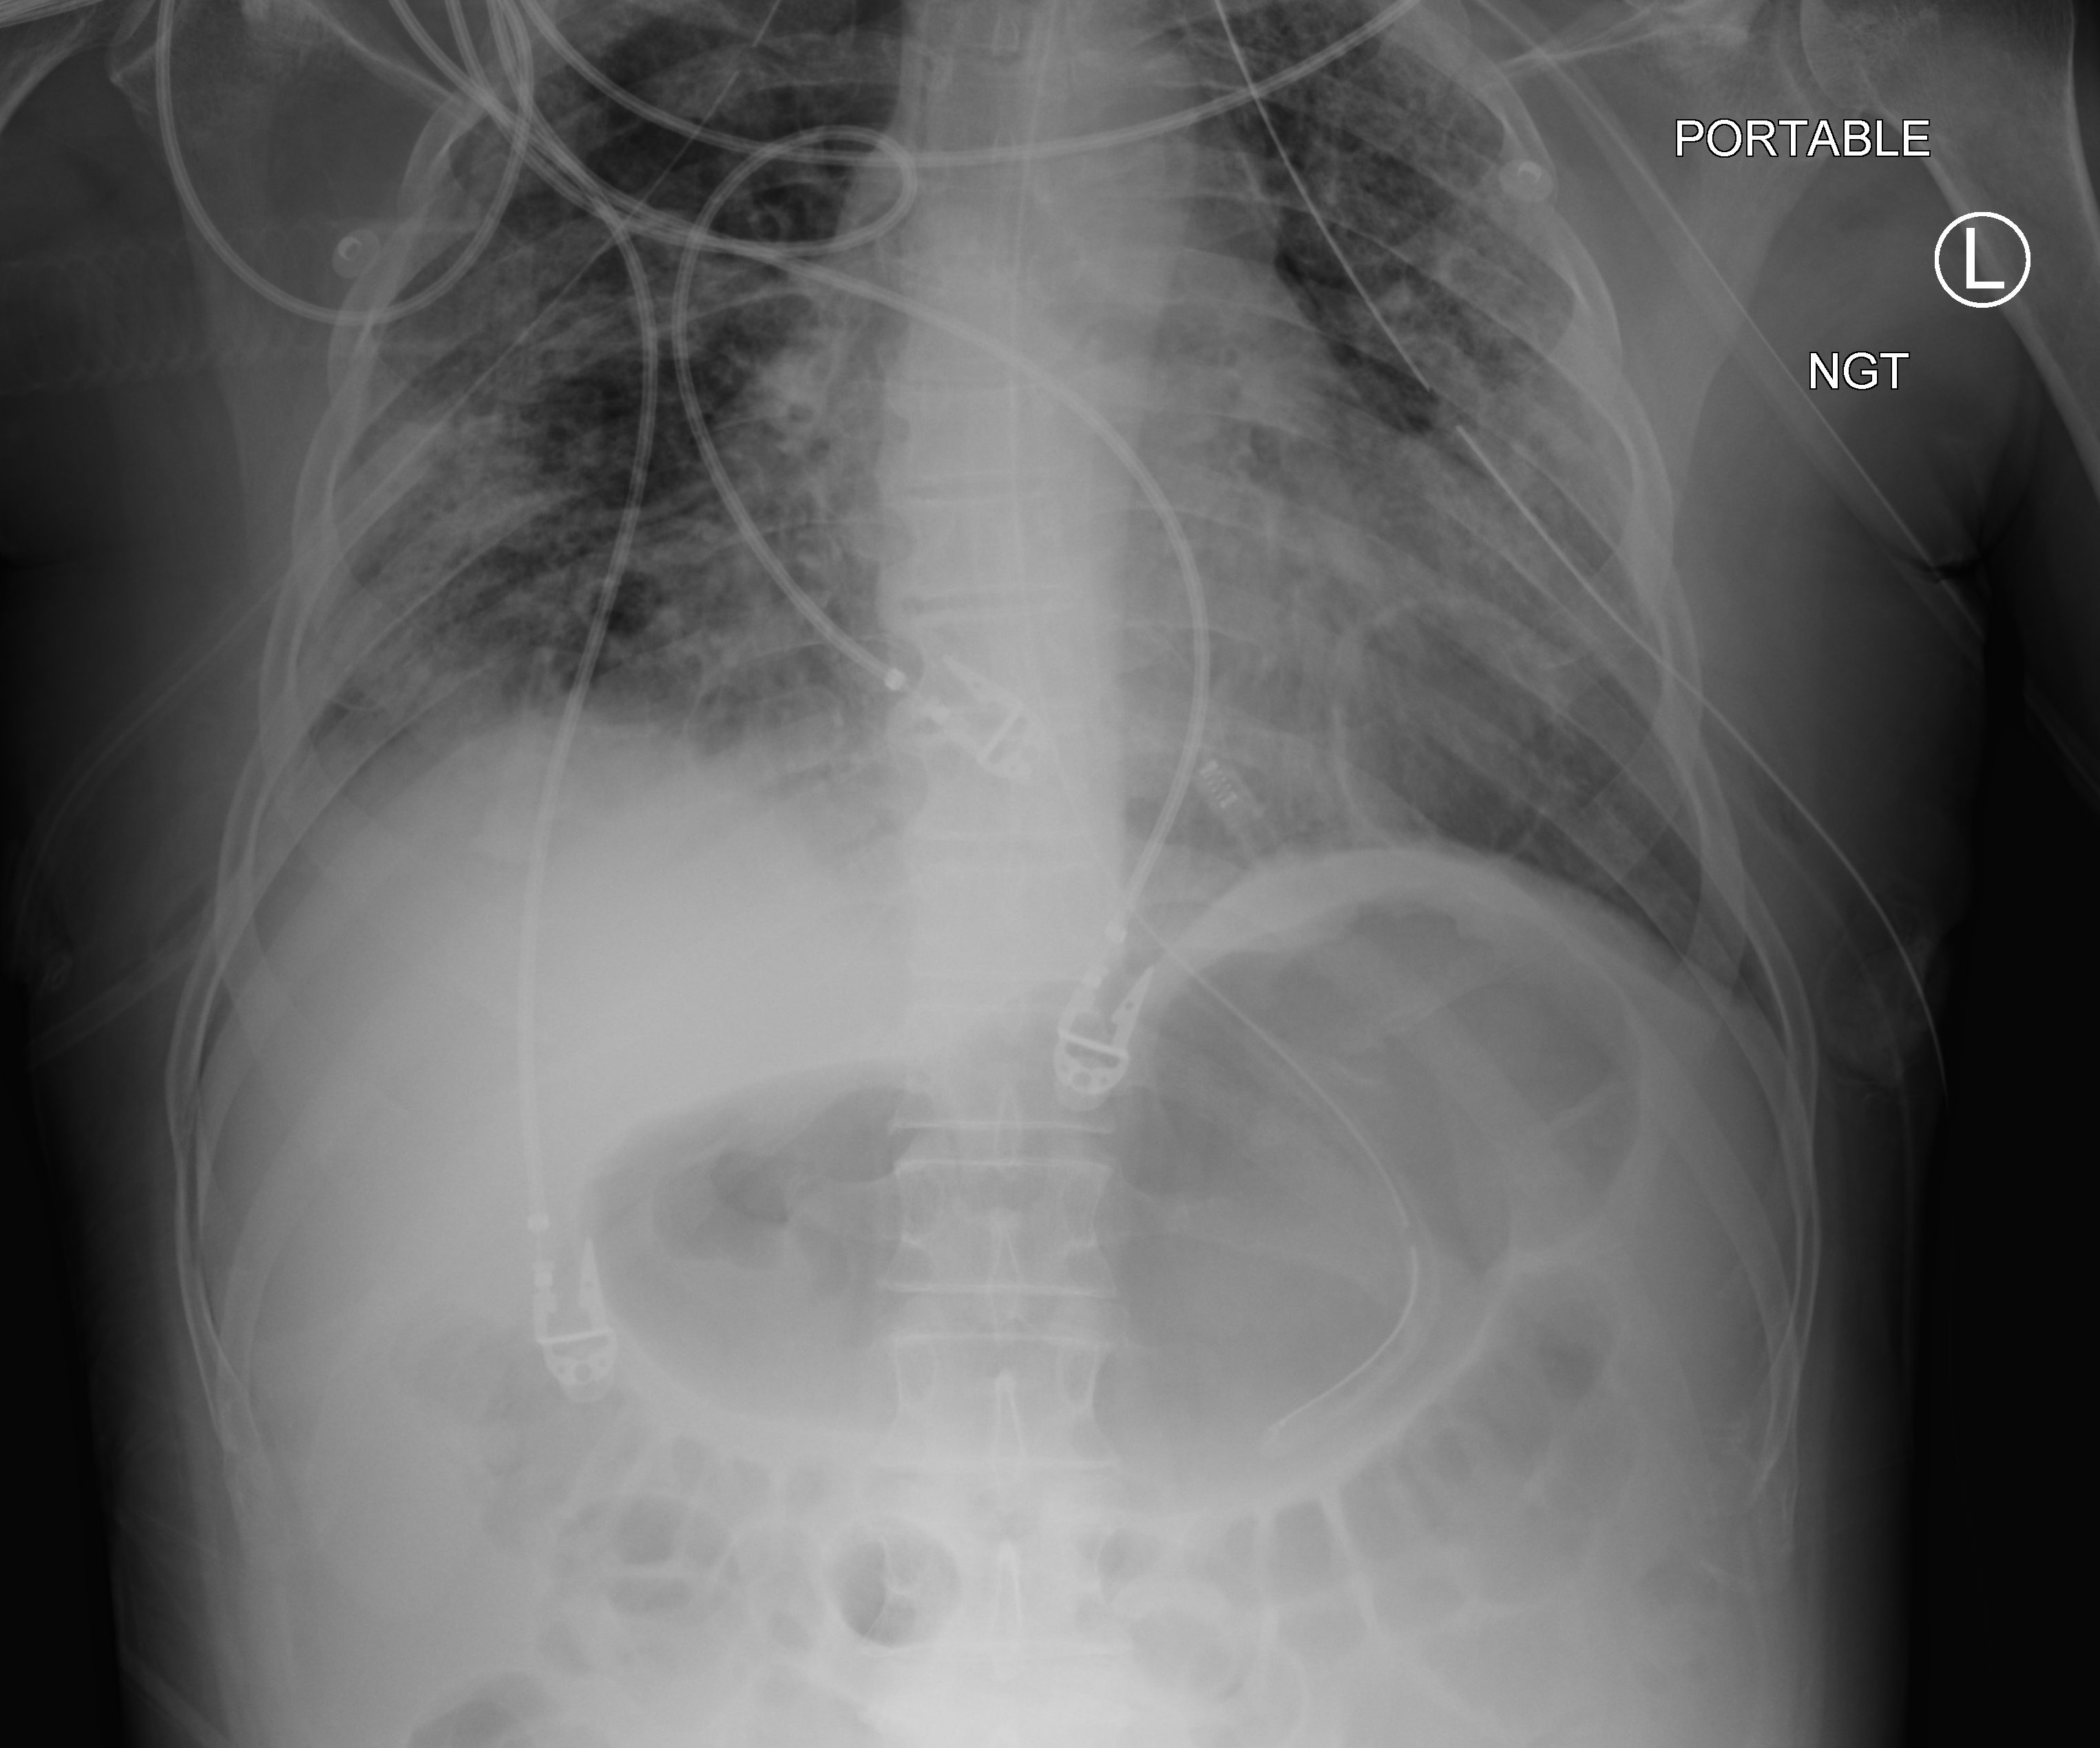
Bedside chest radiograph (computed radiography), anteroposterior (AP) projection. Male patient hospitalised with COVID-19, age 18–59 years.
From the hospital-stay record, not from the radiograph (when in the stay this image was taken is not recorded):
- admitted to intensive care during this hospital stay: yes
- mechanically ventilated during this hospital stay: yes
- length of hospital stay: 83 days